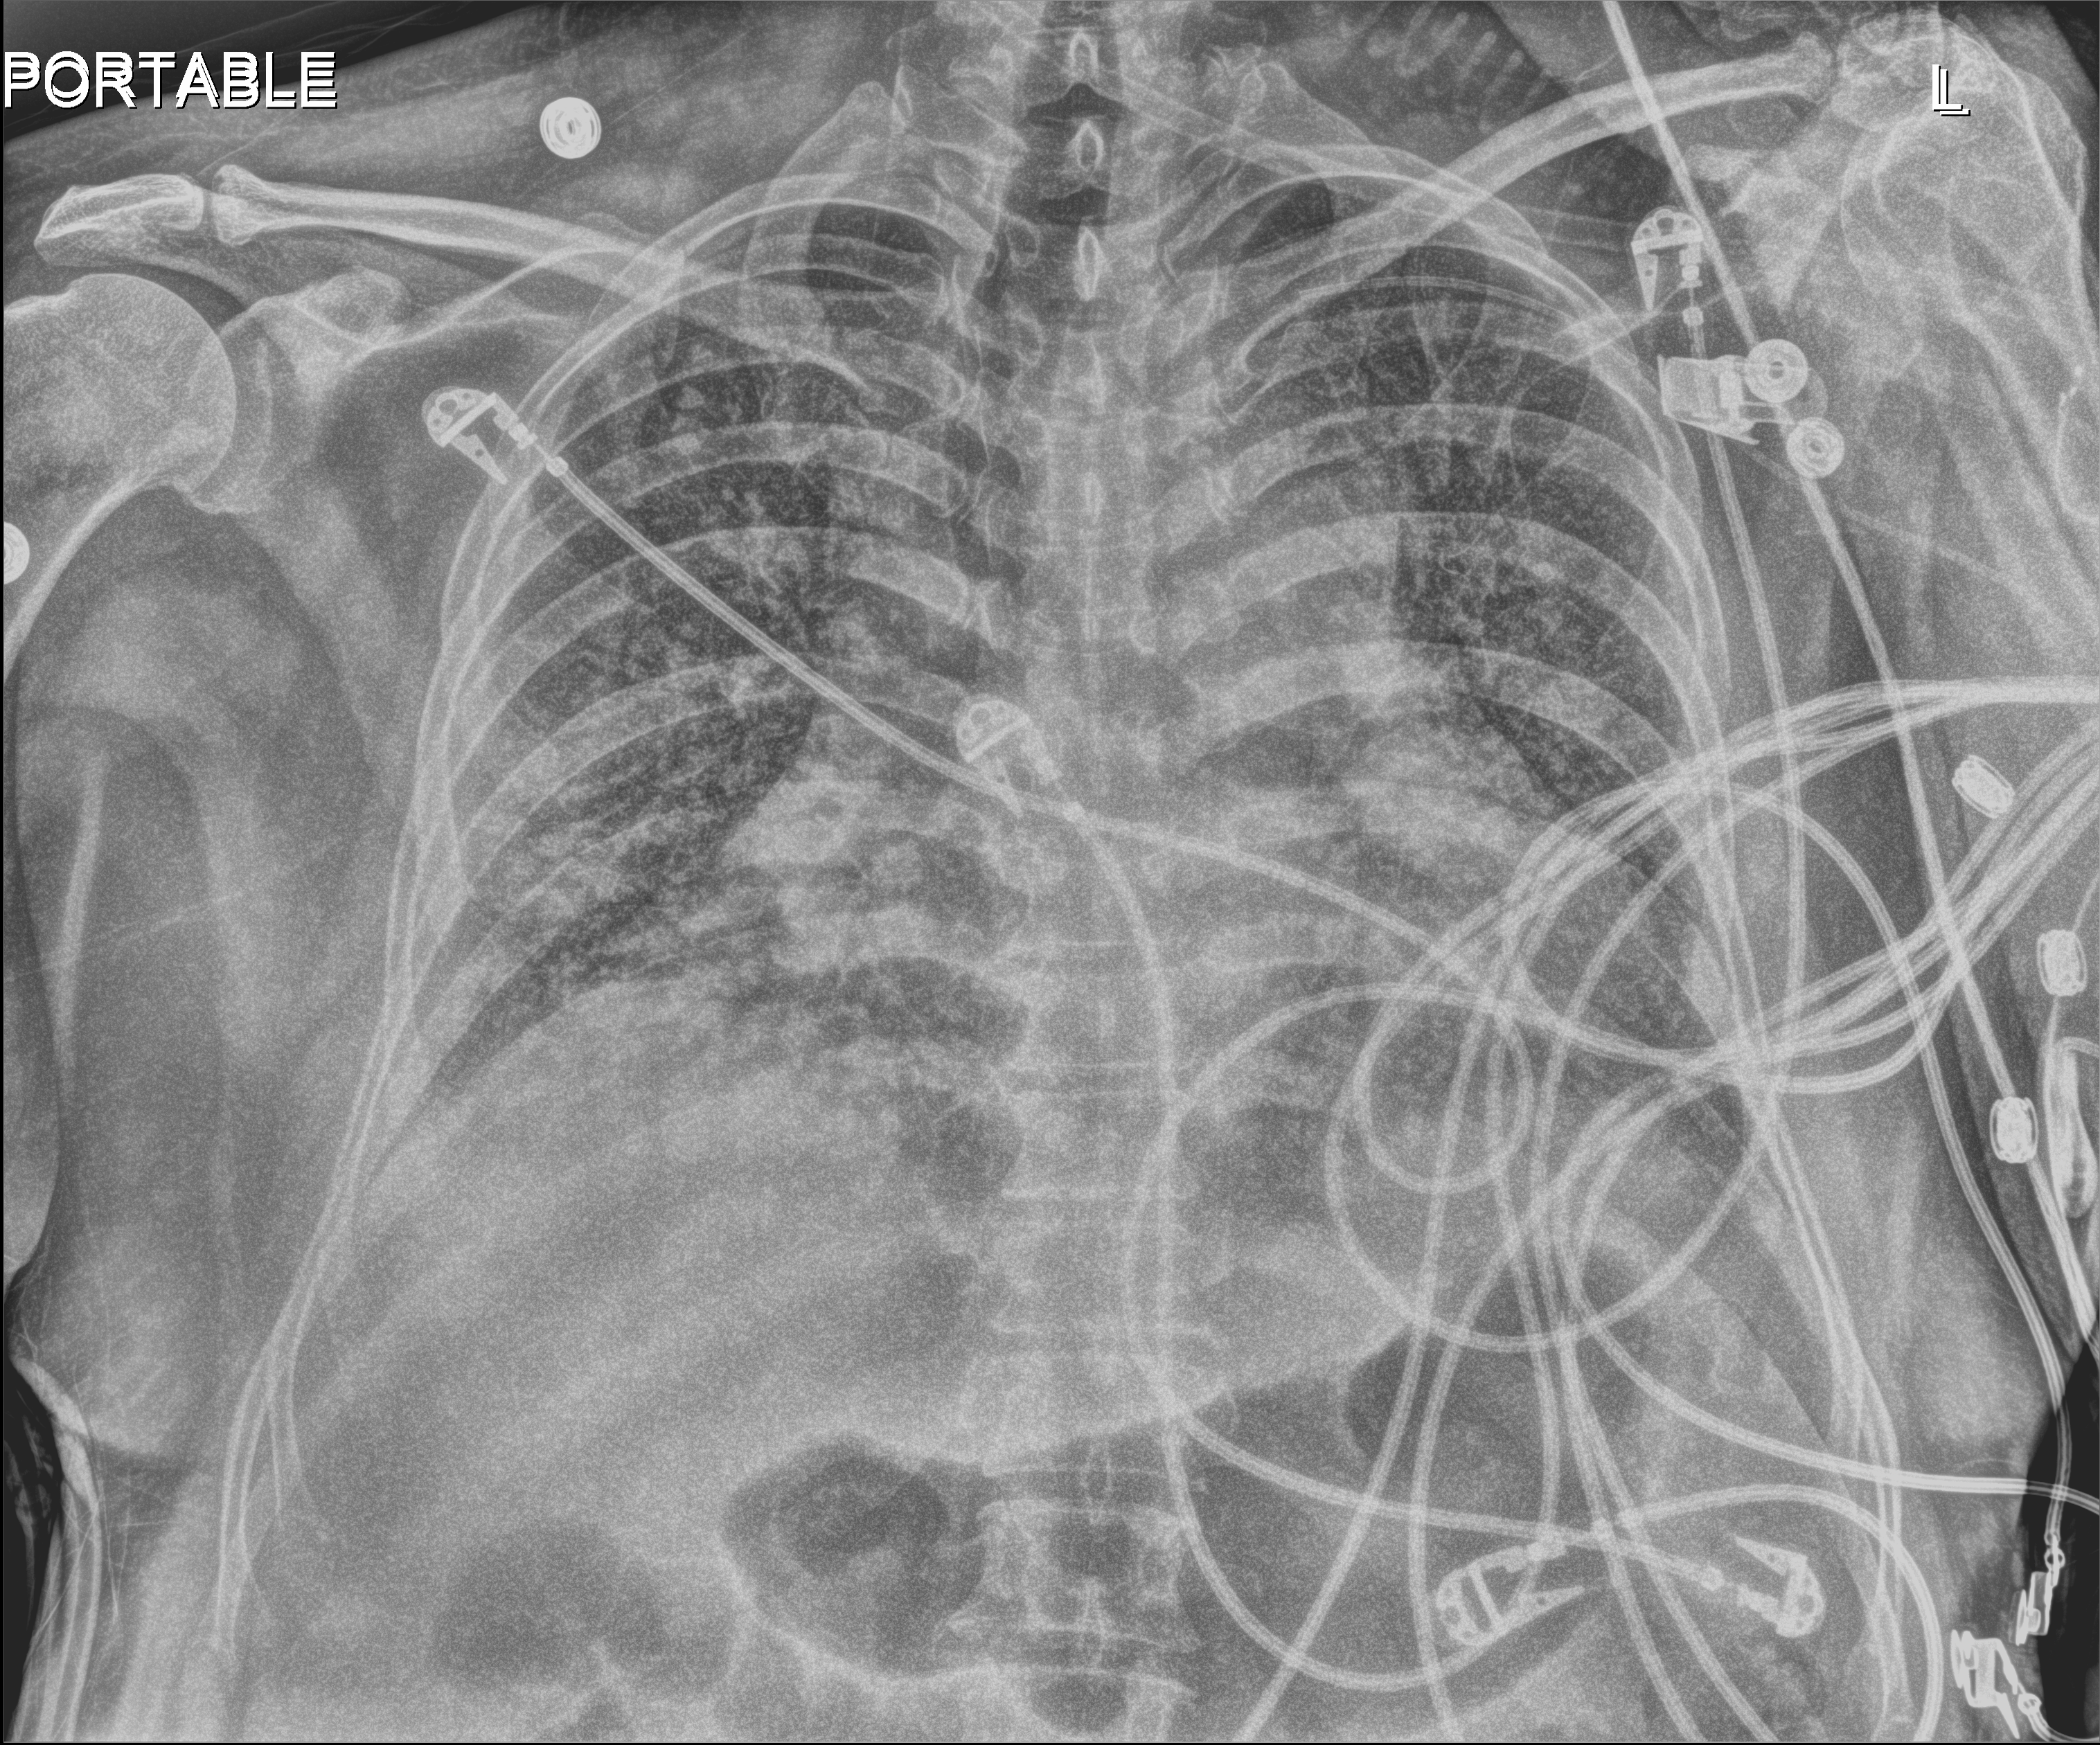
Bedside chest radiograph (digital radiography); anteroposterior (AP) projection. Patient hospitalised with COVID-19, aged 18–59 years.
Admission-level facts for this patient (not findings on this image; timing relative to this image not recorded): smoking status (admission record): never.